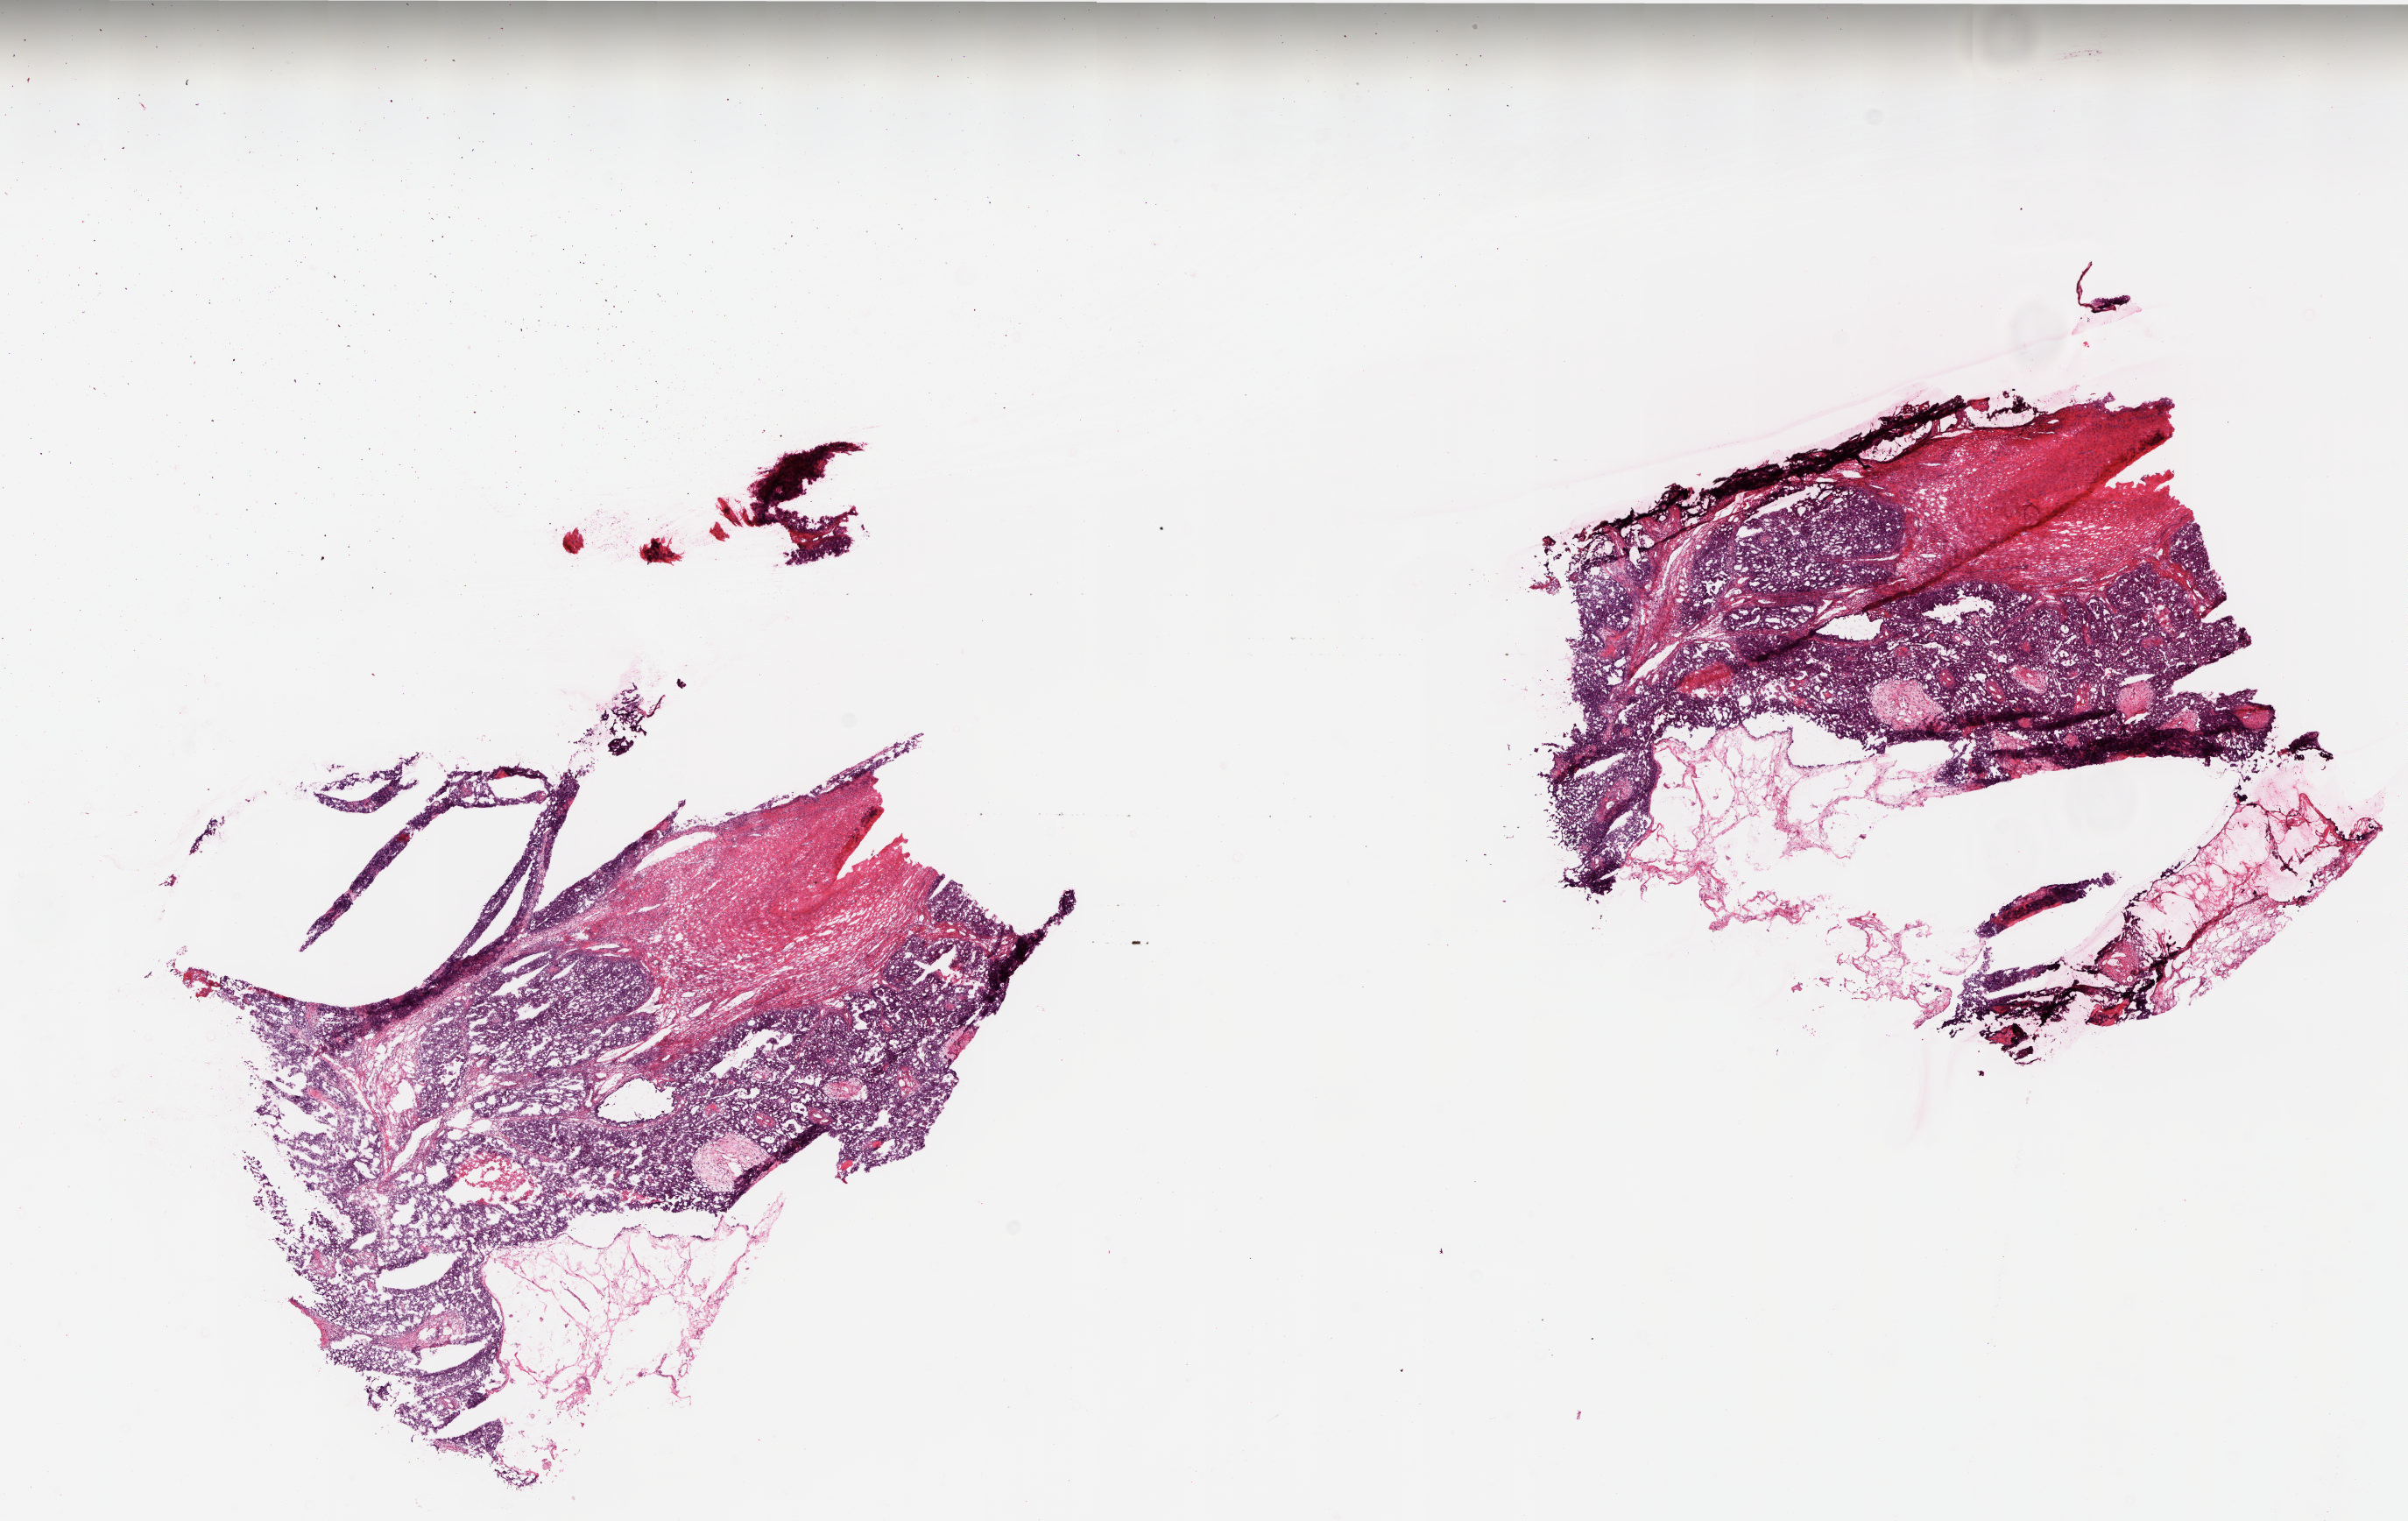
Hematoxylin and eosin (H&E) stained whole-slide image — low-resolution overview of the scanned area, about 22.0 x 13.9 mm. Frozen section. Ovary, primary tumour sample. Patient: female, age at initial diagnosis 65 years.
Histologic diagnosis: Serous cystadenocarcinoma, NOS.